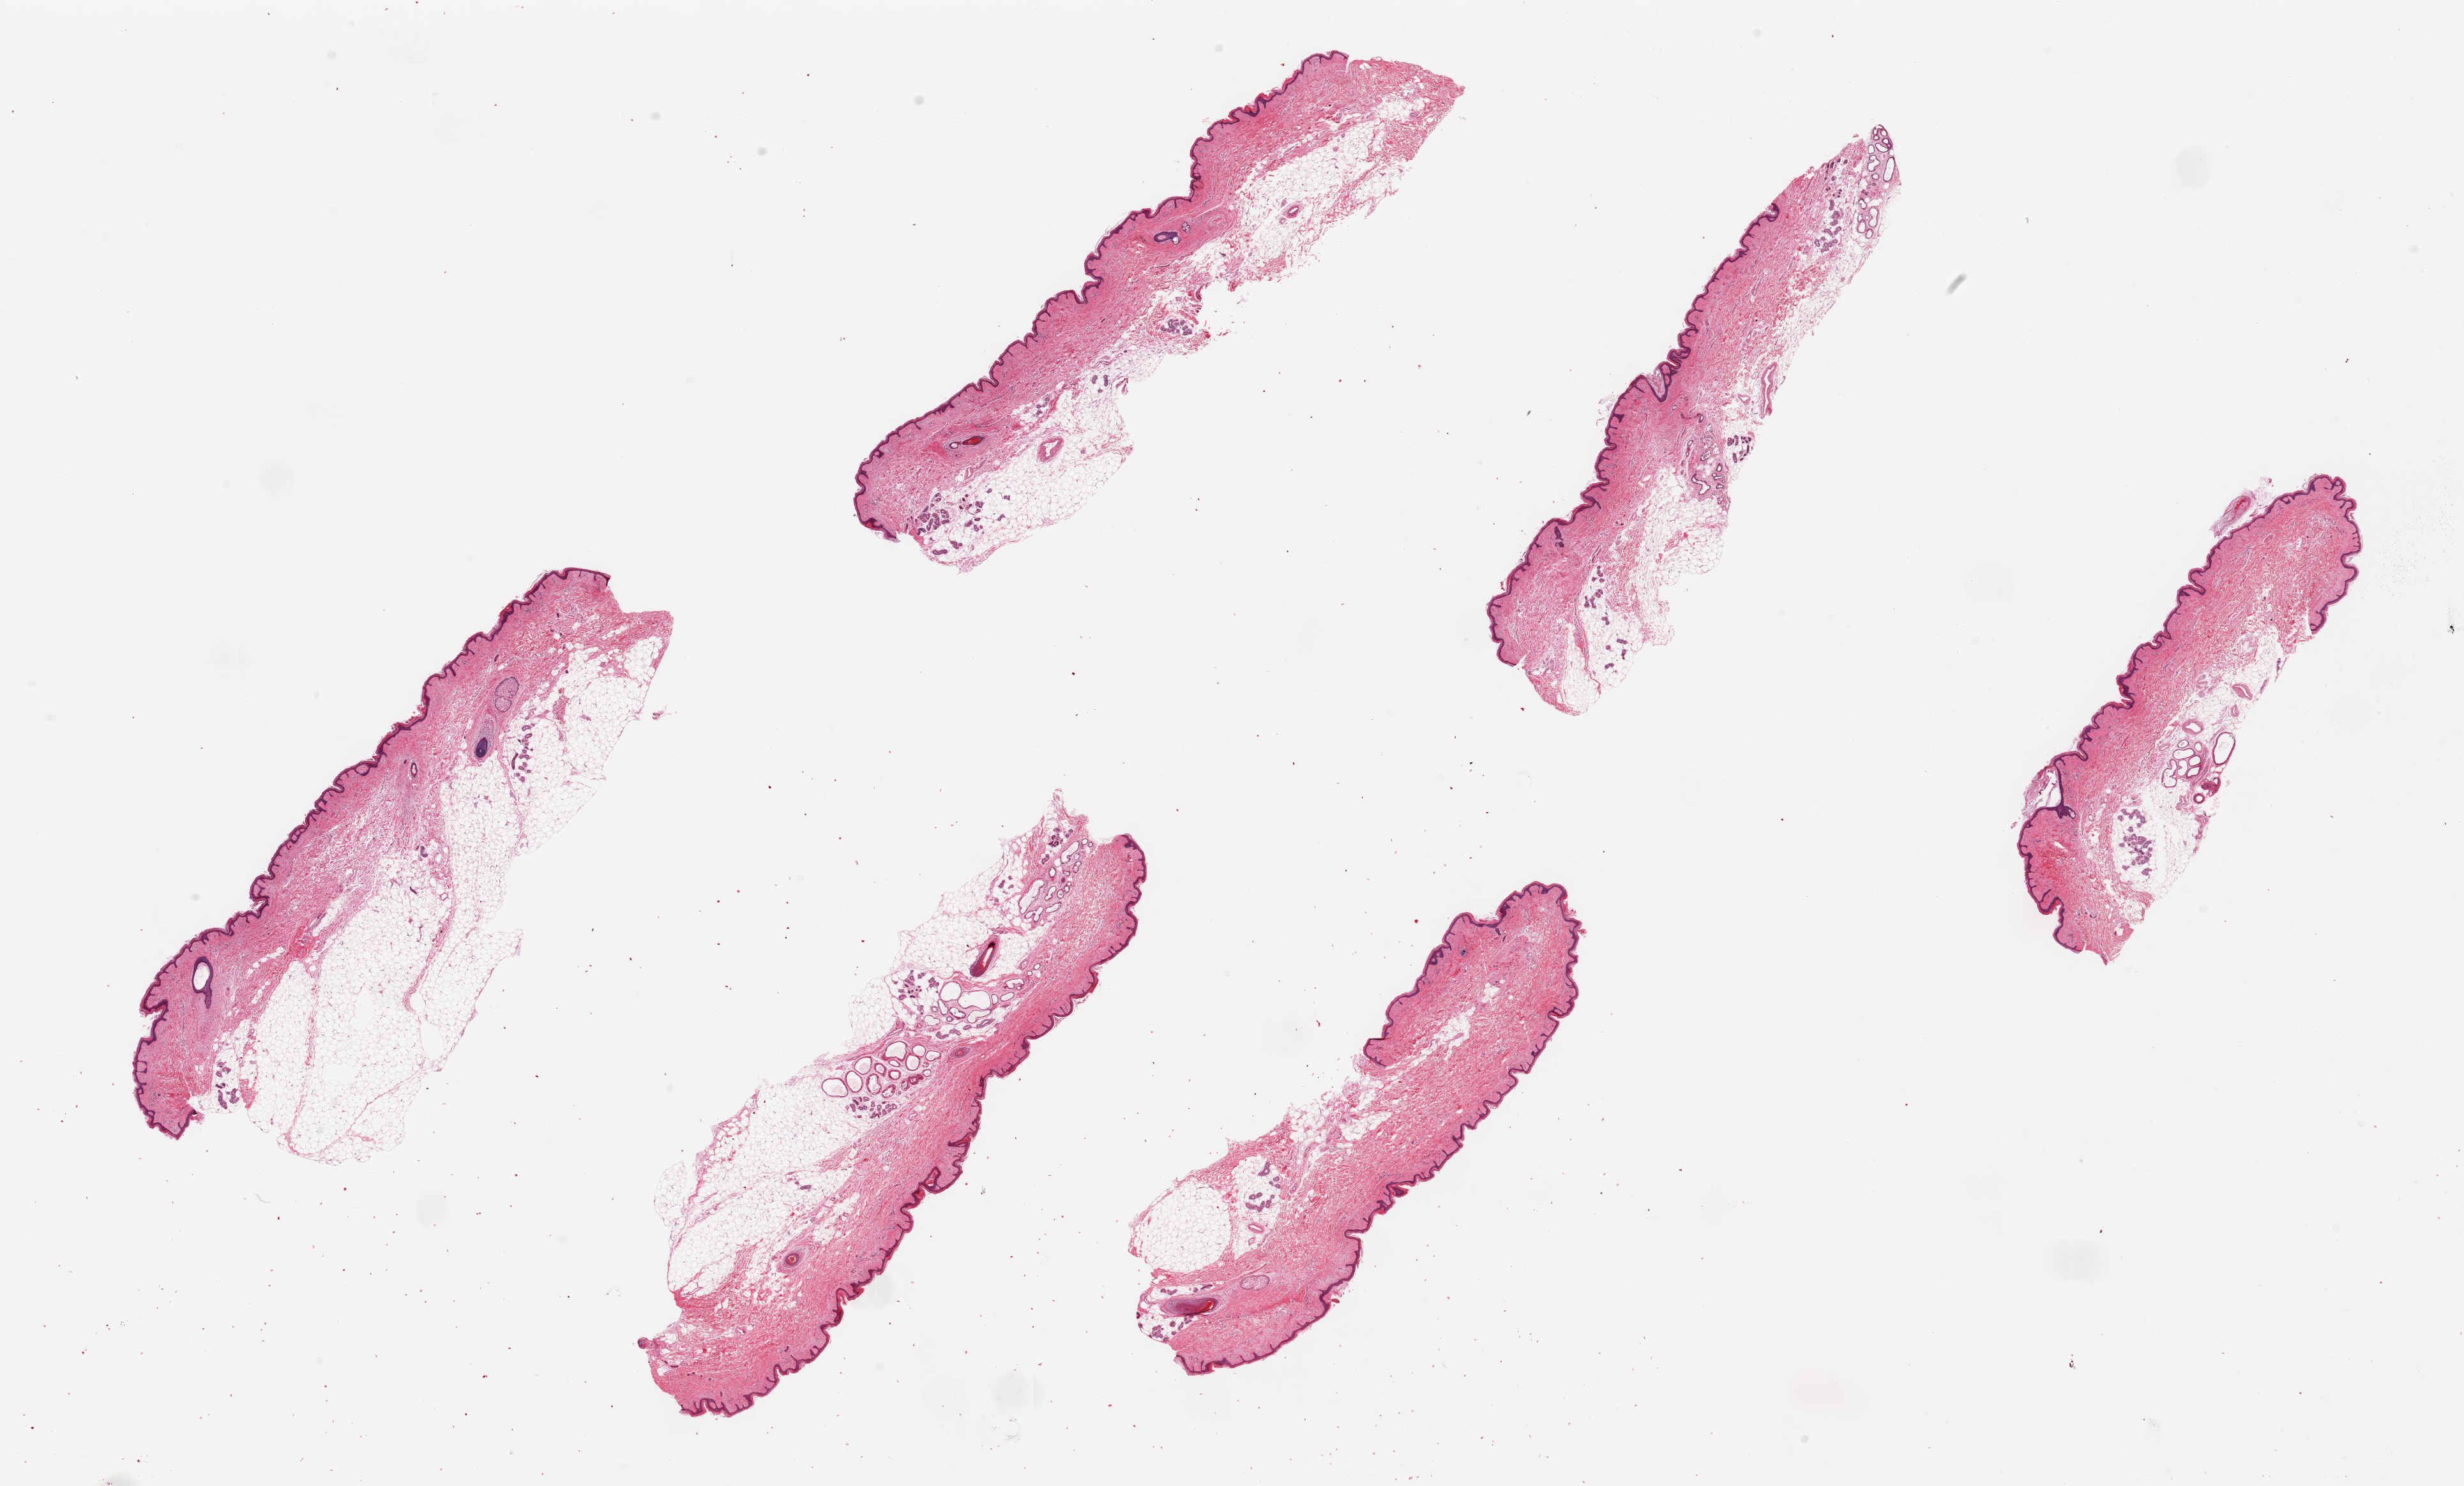
Whole-slide image, hematoxylin and eosin (H&E) stain, a low-resolution overview of the entire scanned area, about 30.5 x 18.4 mm; PAXgene-fixed paraffin-embedded (PFPE) section; target tissue: skin of suprapubic region; tissue donor sample.
- review note (as recorded): 6 pieces, up to 9x3mm; up to 2mm thick subcutaneous adipose